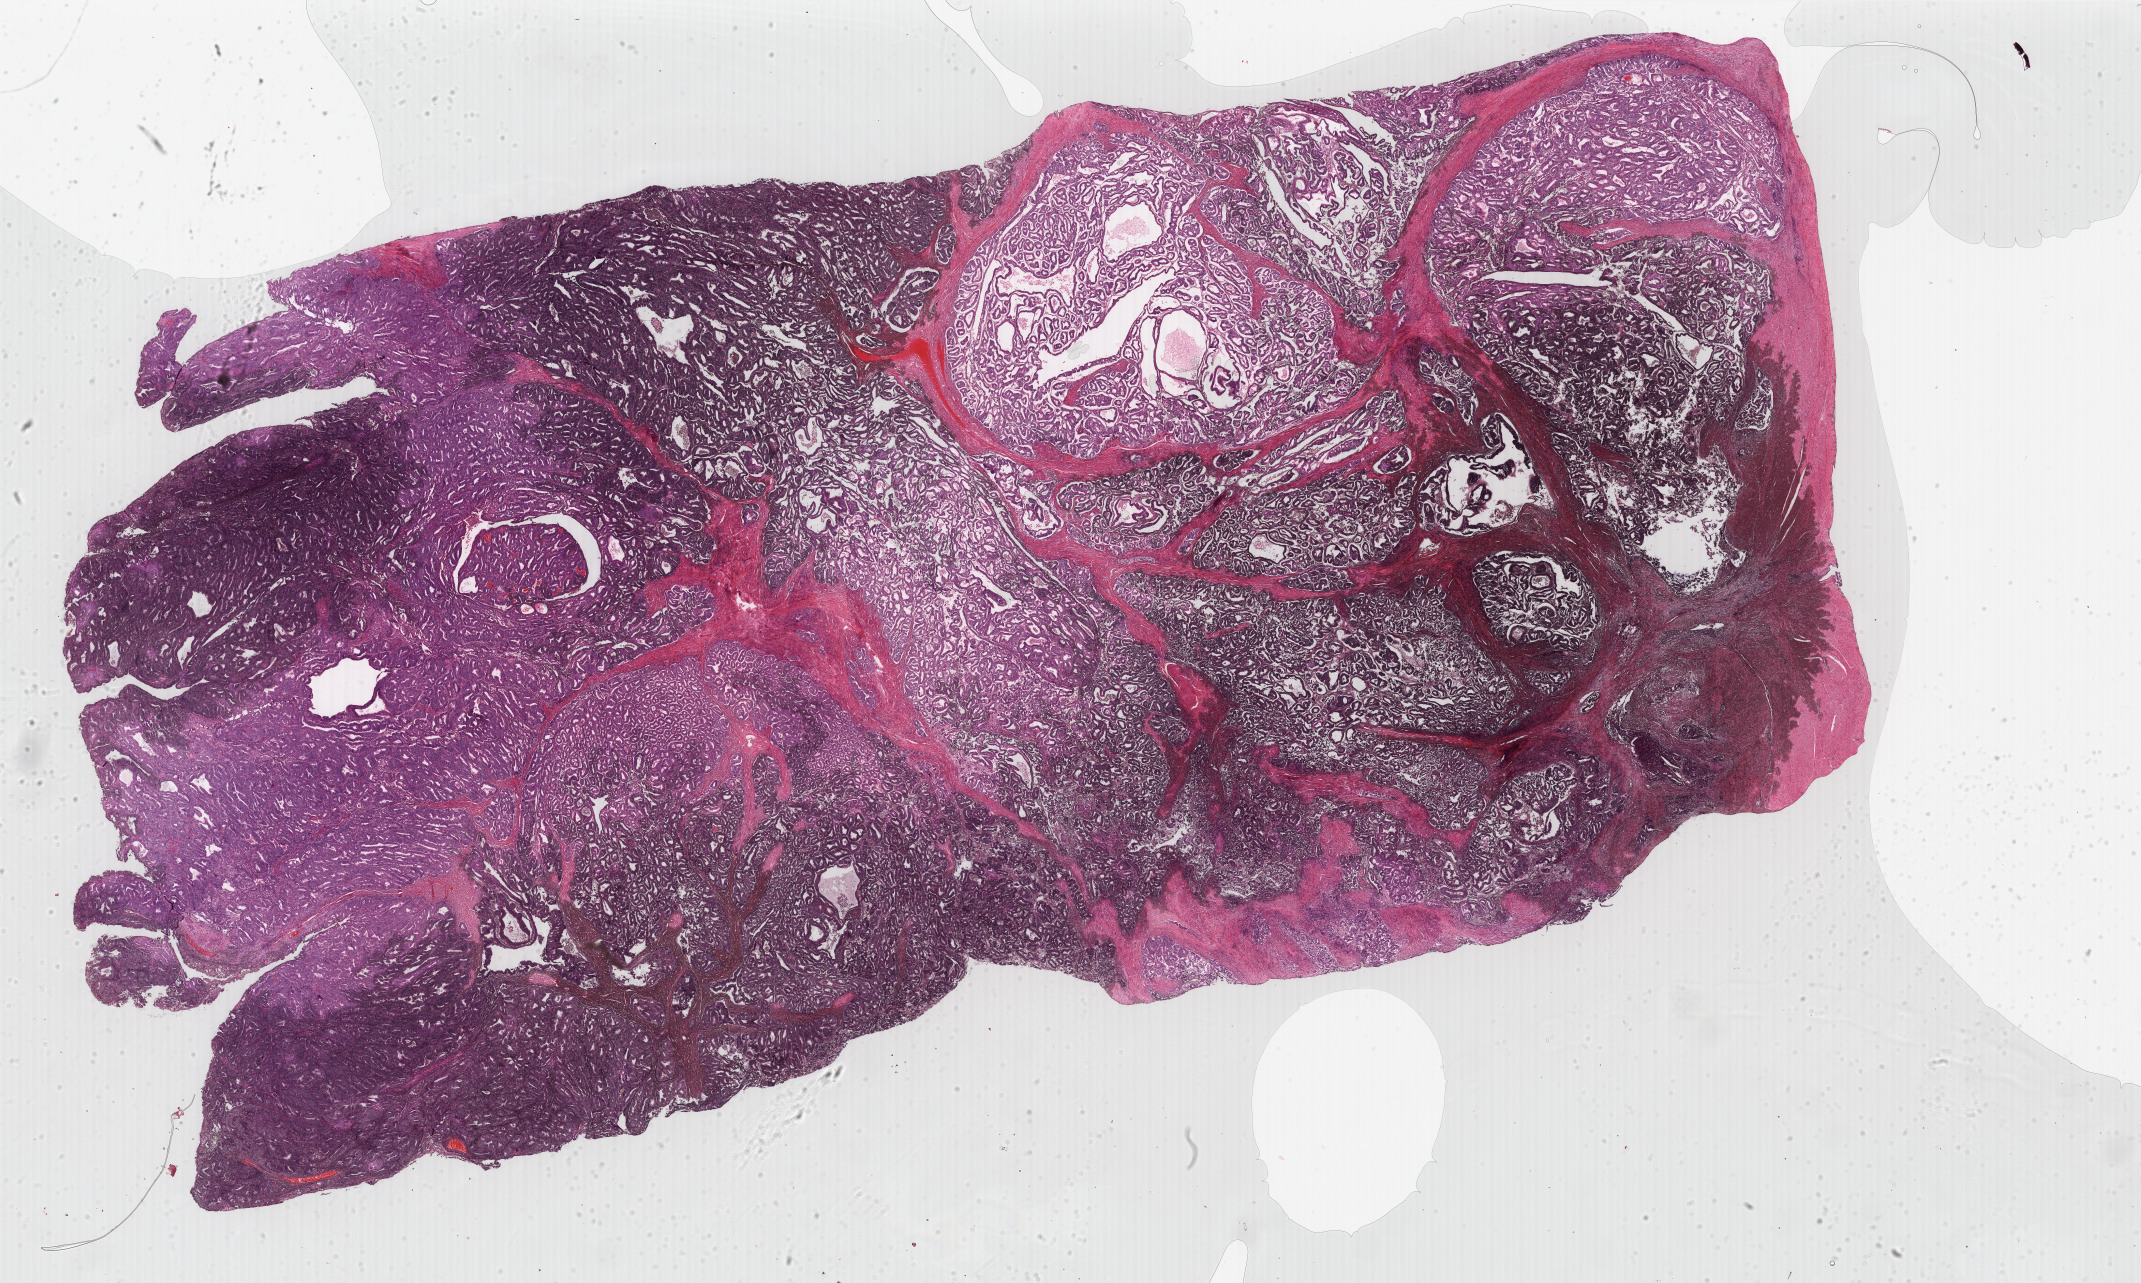
Digitized H&E-stained tissue section (whole slide), whole scanned area (about 34.0 x 20.4 mm, from a 40x scan) shown as a low-resolution overview, formalin-fixed paraffin-embedded (FFPE) diagnostic section, primary tumour sample from the uterus. Female, age 51 years at initial diagnosis. Histologic grade: G2 (moderately differentiated).
Histologic diagnosis: Endometrioid adenocarcinoma, NOS (endometrium). FIGO stage: IA.